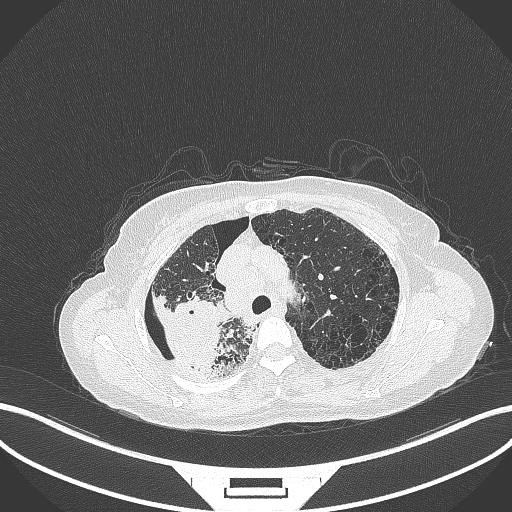
Chest CT, one axial slice; position 265 of 408 along the scan axis; 120 kVp; lung window (W 1500 / L -600 HU); 1 mm slice thickness; 512 × 512 image matrix, field of view 400 × 400 mm. Patient: female, 64 years. Case-level facts recorded for this patient, not image findings: clinical TNM (as recorded): T3 N3 M0.
Outlined on this slice (rectangle marked by the reading radiologist):
- lung tumour (recorded histology: squamous cell carcinoma): bounding box (x1, y1, x2, y2) in pixels: (152, 286, 223, 375)